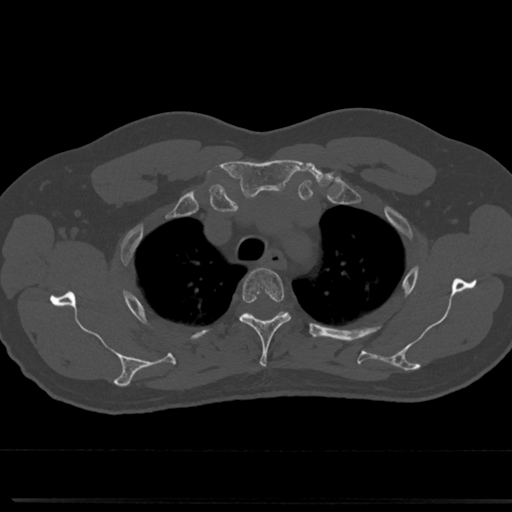
CT including the spine, one axial slice. Slice 585 of 817 in the series (ordered by position). Reconstruction kernel Br40s/3. 120 kVp. Bone window (W 1800 / L 400 HU). 0.5 mm slice thickness. 512 × 512 image matrix, field of view 355 × 355 mm. Patient: male, 61 years. From the clinical record (not read from this slice): primary cancer: prostate.
Annotated regions visible in this slice (semi-automatic segmentation, software-assisted and operator-edited):
- T3 vertebra: bounding box (x1, y1, x2, y2) in pixels: (239, 269, 291, 368)
- T4 vertebra: (242, 311, 306, 339)